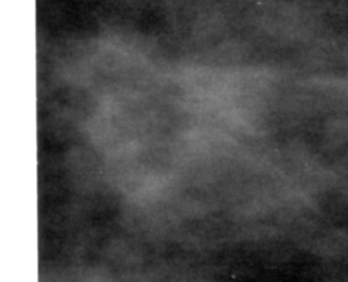
Crop from a digitized film mammogram around one marked abnormality, right breast, CC view.
Mass, shape focal asymmetric density, margins ill defined; BI-RADS assessment category 4; subtlety rating 1 on a 1 (subtle) to 5 (obvious) scale; pathology (as recorded): benign.